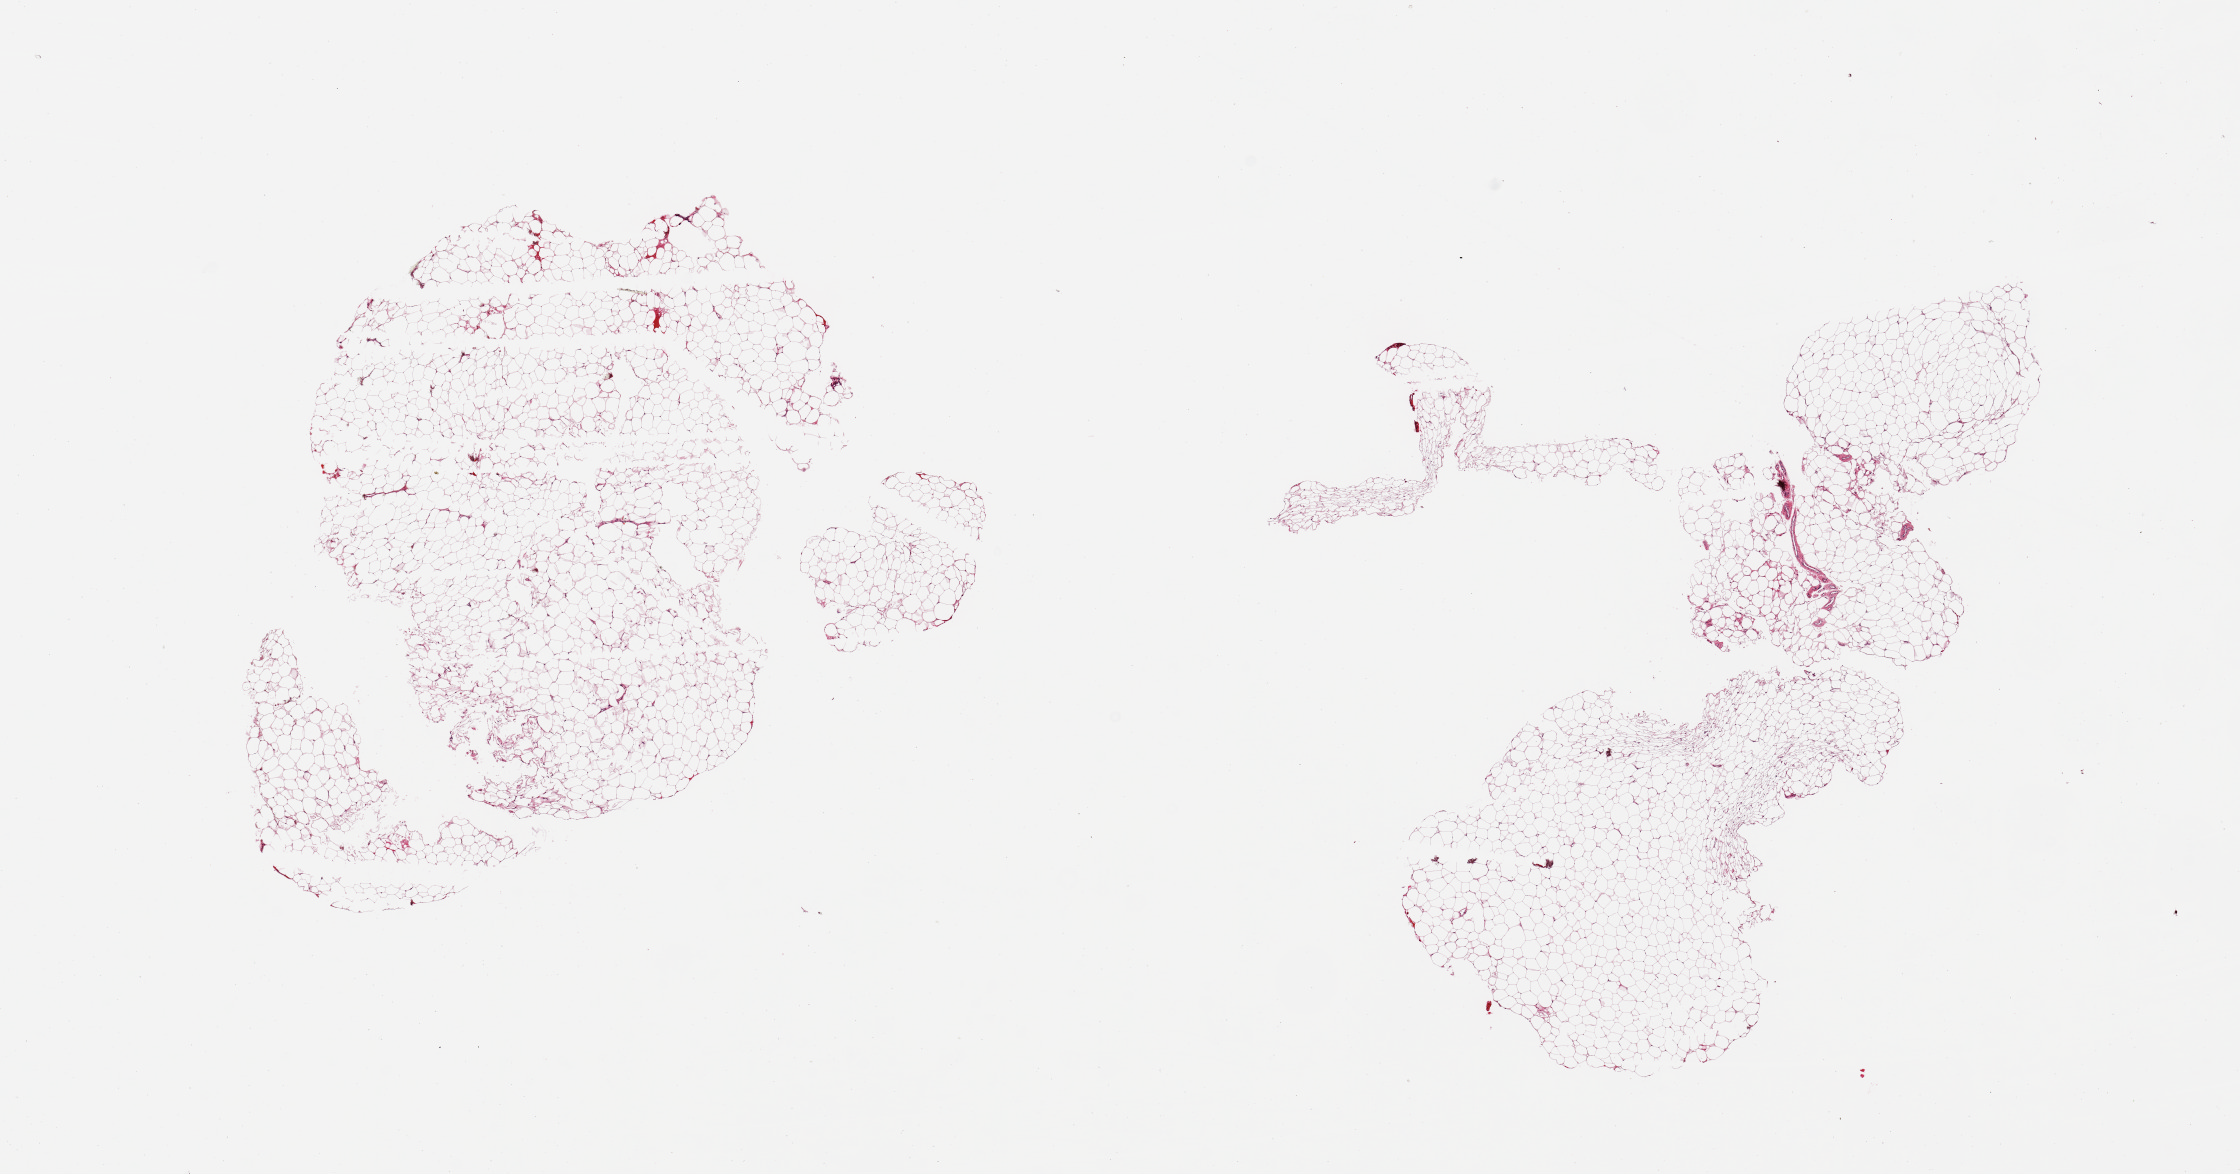
Haematoxylin and eosin whole-slide image — whole scanned area (about 17.7 x 9.3 mm, acquisition: 20x scan) shown as a low-resolution overview. PAXgene-fixed paraffin-embedded (PFPE) section. Section of breast (target tissue). Tissue donor sample.
Reviewer comment on this tissue sample: 2 pieces; no increase in fibrous stroma; no tubules.